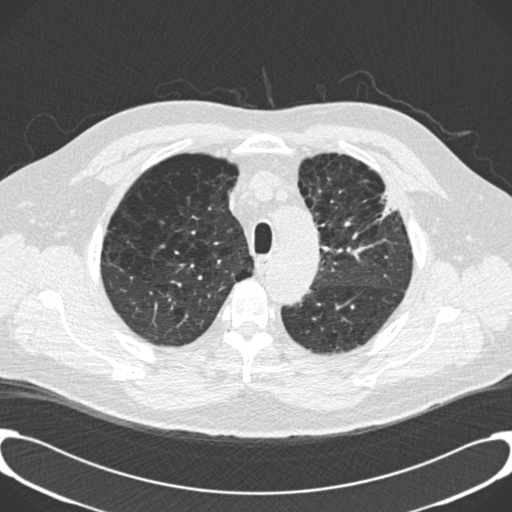
Low-dose screening chest CT, axial slice. Third annual screen. Lung window (W 1500 / L -600 HU). 2 mm slice thickness. Standard (soft-tissue) reconstruction kernel (B30f). Slice 35 of 189 in the series. Male, age 59 years at enrolment. Current smoker at enrolment.
Expert-annotated lung lesion, bounding box (x1, y1, x2, y2) in pixels: (363, 175, 410, 230). No non-calcified nodule or mass ≥4 mm was recorded by the screening reader at this exam. Official screen result: positive, other. Later outcome: lung cancer diagnosed 134 days after this screen — bronchiolo-alveolar carcinoma, mixed mucinous and non-mucinous, left upper lobe, stage IA (AJCC 6th edition), 20 mm at pathology.